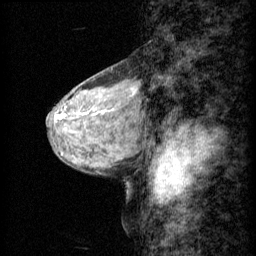
Breast MRI (dynamic contrast-enhanced), one sagittal slice; slice 23 of 60 in the series (ordered by position); 3 images stored at this slice position (order not interpretable as contrast timing); 1.5 T; TE 4.2 ms, TR 11 ms; 1.5 mm slice thickness; 256 × 256 image matrix, field of view 200 × 200 mm. Female patient, age 48 years.
Annotated regions visible in this slice (semi-automatic segmentation, software-assisted and operator-edited):
- analysis volume of interest (the breast-tissue region the enhancement analysis was run in; not a lesion): bounding box (x1, y1, x2, y2) in pixels: (61, 76, 141, 143)
- tumour enhancement mask (voxels above the 70 % enhancement threshold inside the analysis volume of interest): (133, 90, 136, 95)